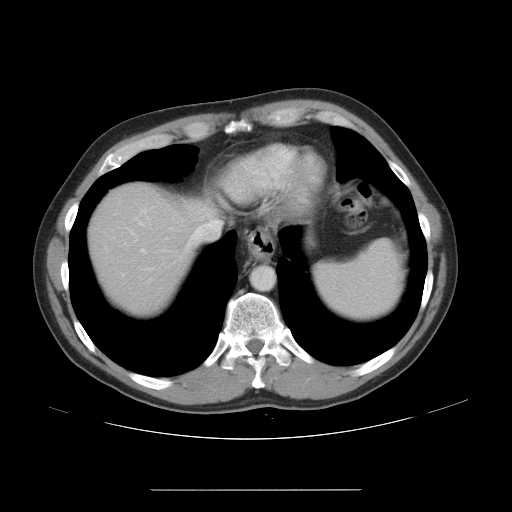
Contrast-enhanced abdominal CT, one axial slice; position 39 of 48 along the scan axis; reconstruction kernel STANDARD; 120 kVp; soft-tissue window (W 400 / L 40 HU); 5 mm slice thickness; 512 × 512 image matrix, field of view 409 × 409 mm. Male patient, age 56 years. Case-level facts recorded for this patient, not image findings: diagnosis: colorectal cancer liver metastases, imaged before liver resection; multiple liver metastases: yes; largest metastasis: 1.8 cm; disease in both lobes: yes.
Structures marked on this image (outlined manually by an expert reader):
- hepatic veins: bounding box (x1, y1, x2, y2) in pixels: (187, 220, 220, 247)
- liver: (91, 186, 192, 313)
- planned liver remnant (the part of the liver to remain after resection): (91, 186, 192, 313)